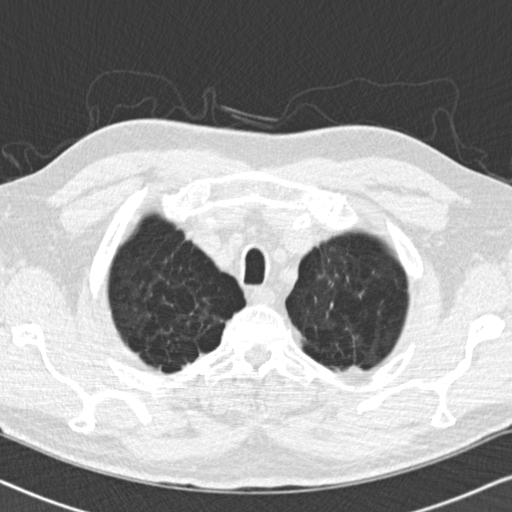
Low-dose screening chest CT, one axial slice. Position 157 of 175 along the scan axis. 120 kVp. Lung window (W 1500 / L -600 HU). 2 mm slice thickness. 512 × 512 image matrix.
Annotated regions visible in this slice (expert manual segmentation):
- lesion 1 (tumor, upper lobe of left lung): bounding box (x1, y1, x2, y2) in pixels: (344, 365, 363, 373)